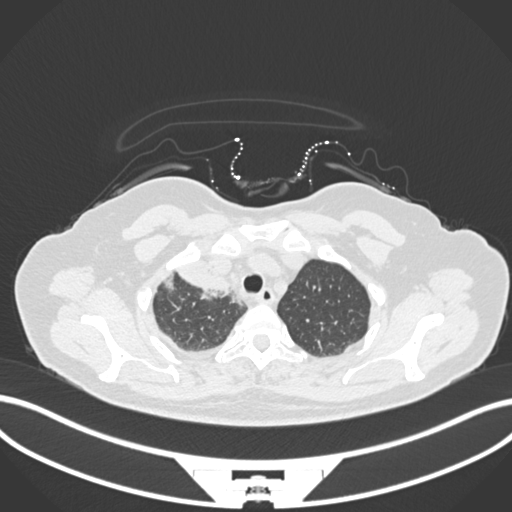
Chest CT, one axial slice; slice 142 of 172 in the series (ordered by position); 120 kVp; lung window (W 1500 / L -600 HU); 512 × 512 image matrix. Female patient, age 52 years. From the clinical record (not read from this slice): clinical TNM (as recorded): T3 N1 M1.
Annotated regions visible in this slice (bounding box drawn by a radiologist):
- lung tumour (recorded histology: adenocarcinoma): bounding box [x1, y1, x2, y2] px = [174, 262, 235, 300]